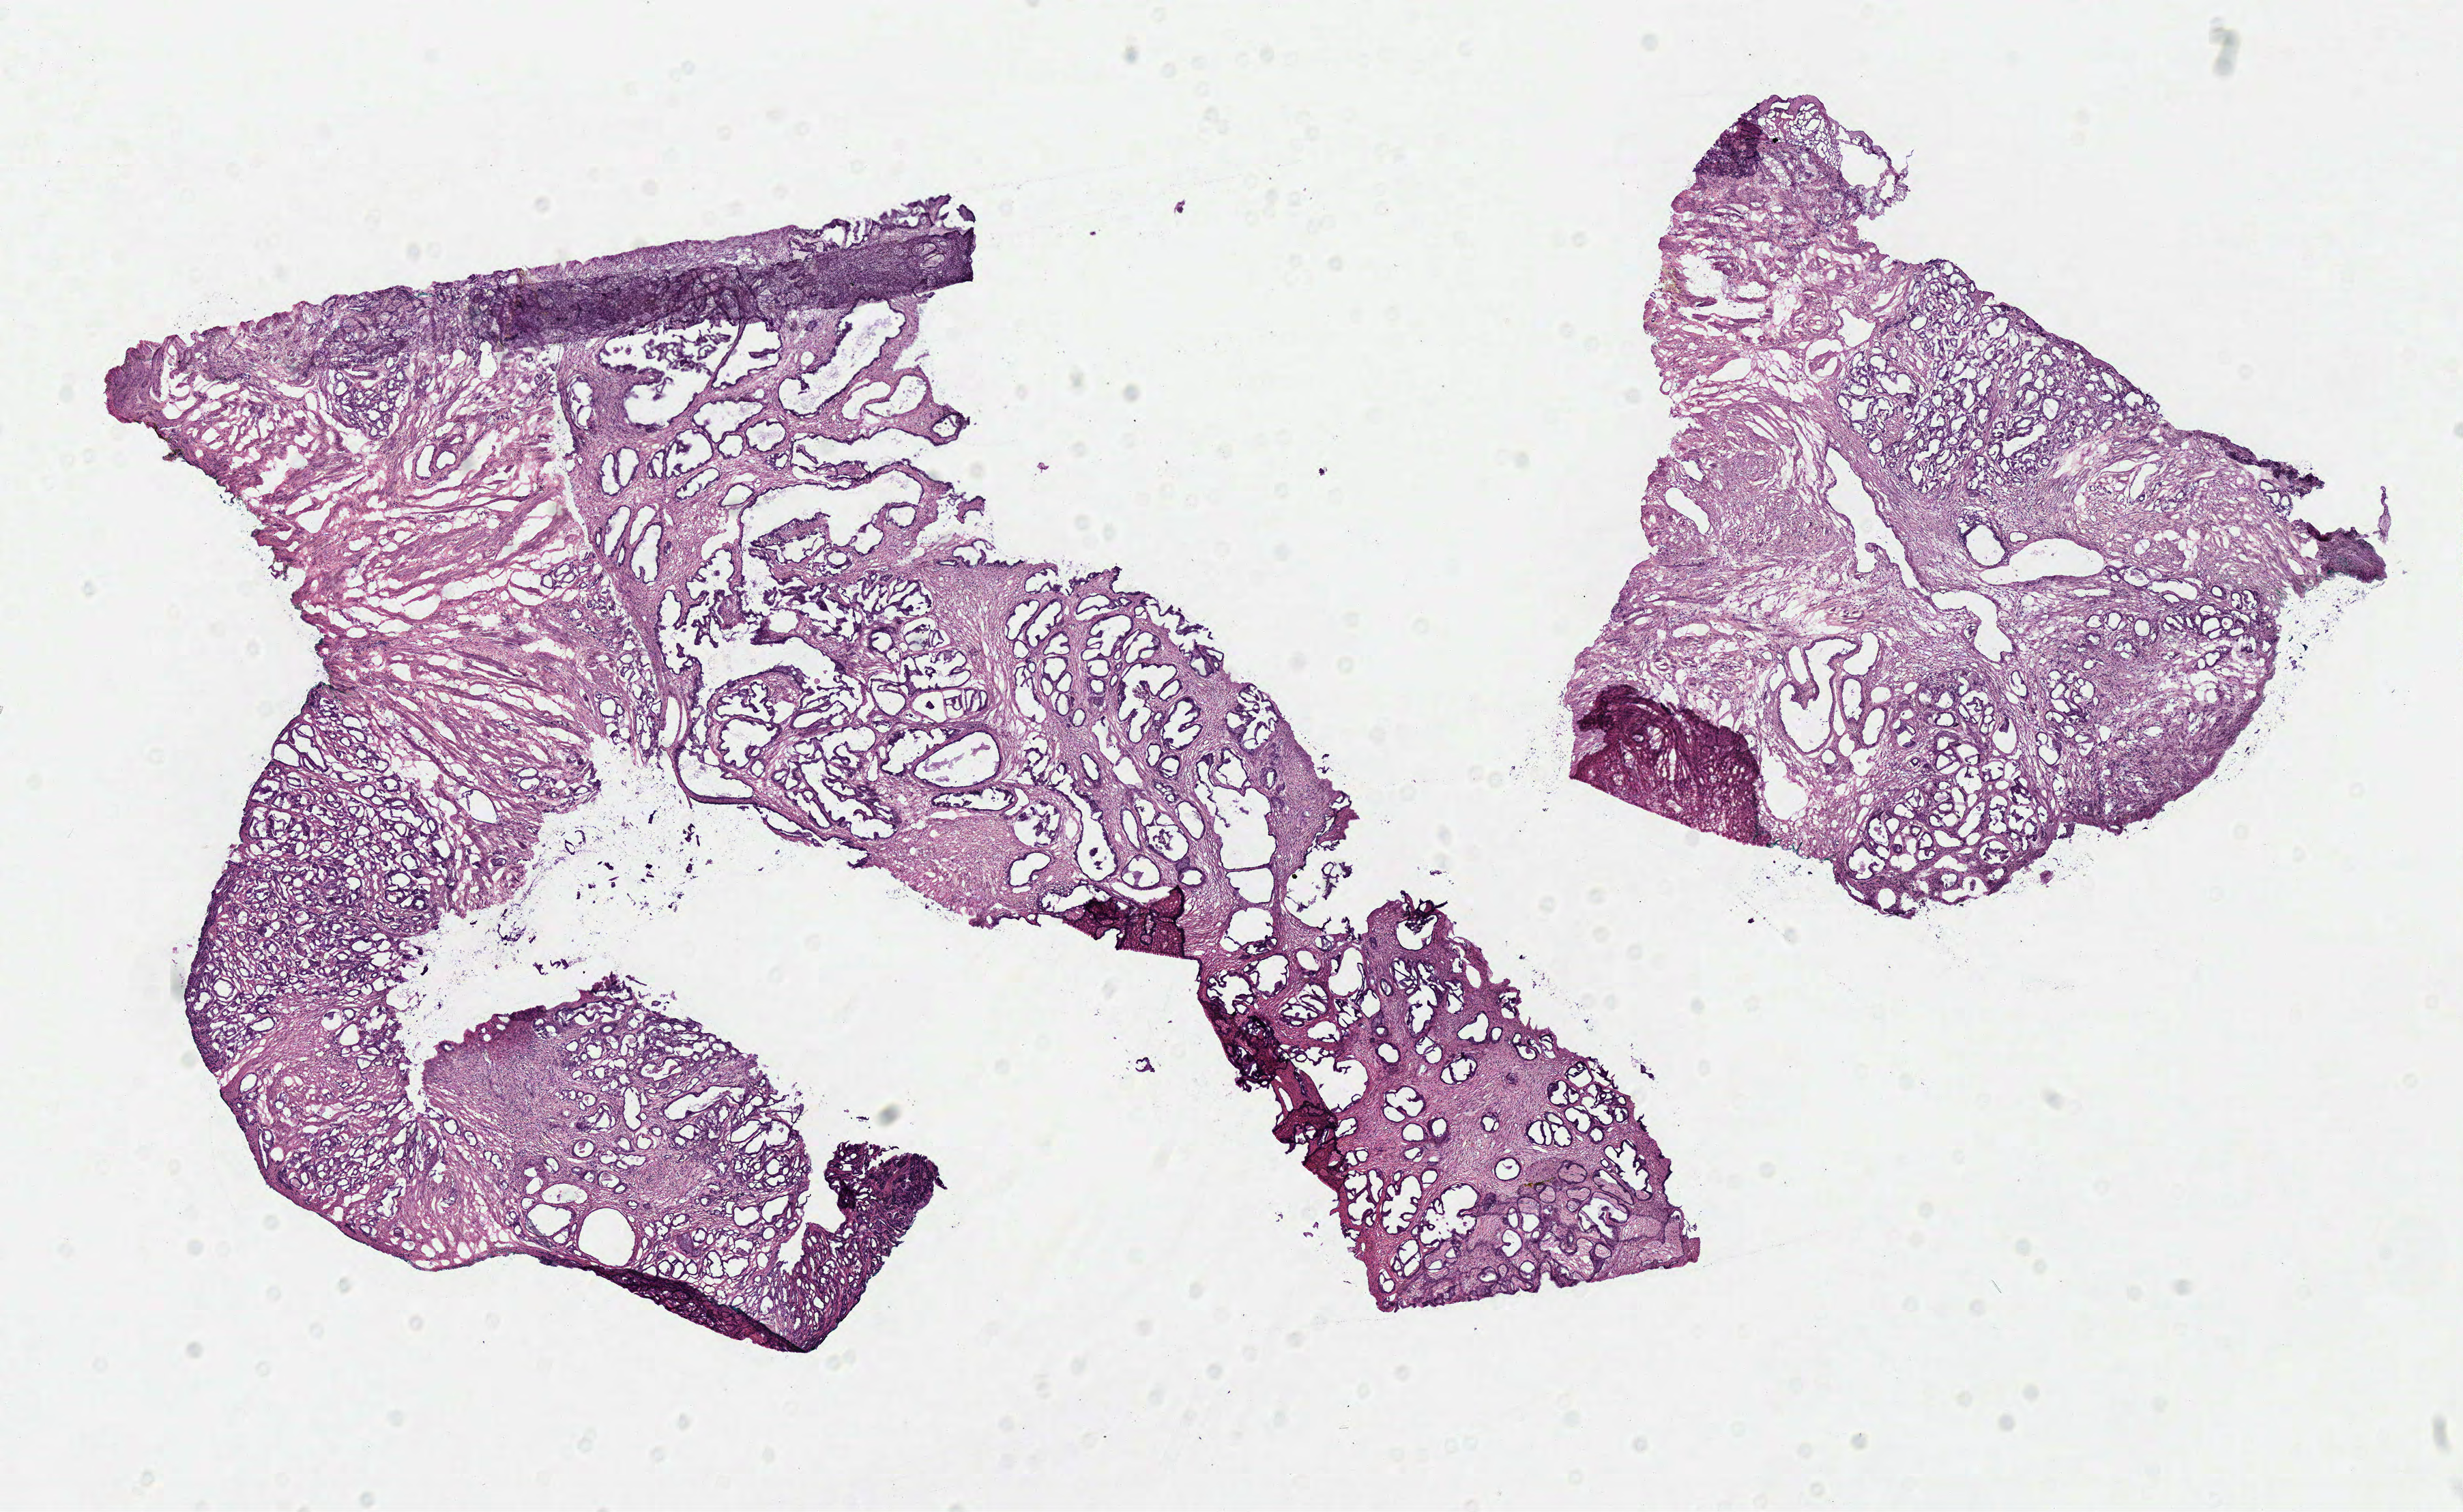
Whole-slide histology image, Hematoxylin and eosin (H&E) stained — low-resolution overview of the scanned area, about 14.2 x 8.7 mm (acquisition: 40x scan), frozen section from the top of the tissue portion, prostate, primary tumour sample. Patient: male, age at initial diagnosis 59 years. Gleason score: 6 (3+3). Pathologist review of this section (percent, as recorded): tumour cells 70%, tumour nuclei 60%, normal cells 30%, stromal cells 0%, necrosis 0%. Inflammatory infiltration, as recorded: lymphocyte infiltration 0%, monocyte infiltration 0%, neutrophil infiltration 0%.
- diagnosis: Adenocarcinoma, NOS (prostate gland)